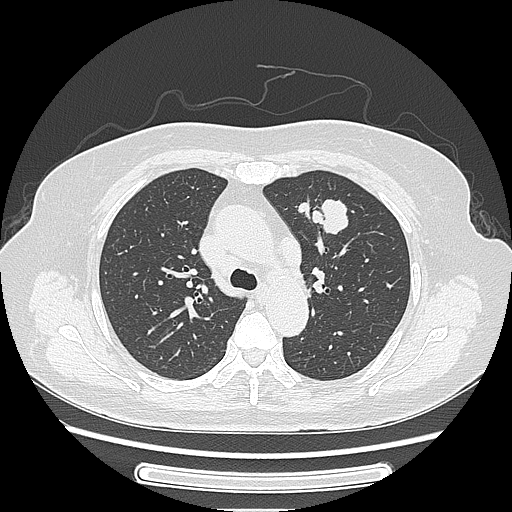
Chest CT, one axial slice; slice 167 of 227 in the series (ordered by position); reconstruction kernel LUNG; lung window (W 1500 / L -600 HU); 1.25 mm slice thickness; 512 × 512 image matrix, field of view 363 × 363 mm. Female patient, age 77 years. Case-level facts recorded for this patient, not image findings: clinical TNM (as recorded): T1c N3 M0.
Outlined on this slice (bounding box drawn by a radiologist):
- lung tumour (recorded histology: adenocarcinoma): bounding box [x1, y1, x2, y2] px = [314, 192, 363, 239]